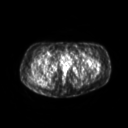
FDG PET of an extremity soft-tissue mass (from a PET/CT study), one axial slice. Position 44 of 267 along the scan axis. 3.27 mm slice thickness. 128 × 128 image matrix. Patient: female, 60 years. Case-level facts recorded for this patient, not image findings: histological type: spindle cell suggestive of myxofibrosarcoma; grade: intermediate; site of the primary tumour: right buttock.
Annotated regions visible in this slice (expert contour drawn on MRI and transferred to this co-registered scan by the dataset authors):
- gross tumour volume (mass): bounding box (x1, y1, x2, y2) in pixels: (34, 73, 37, 77)